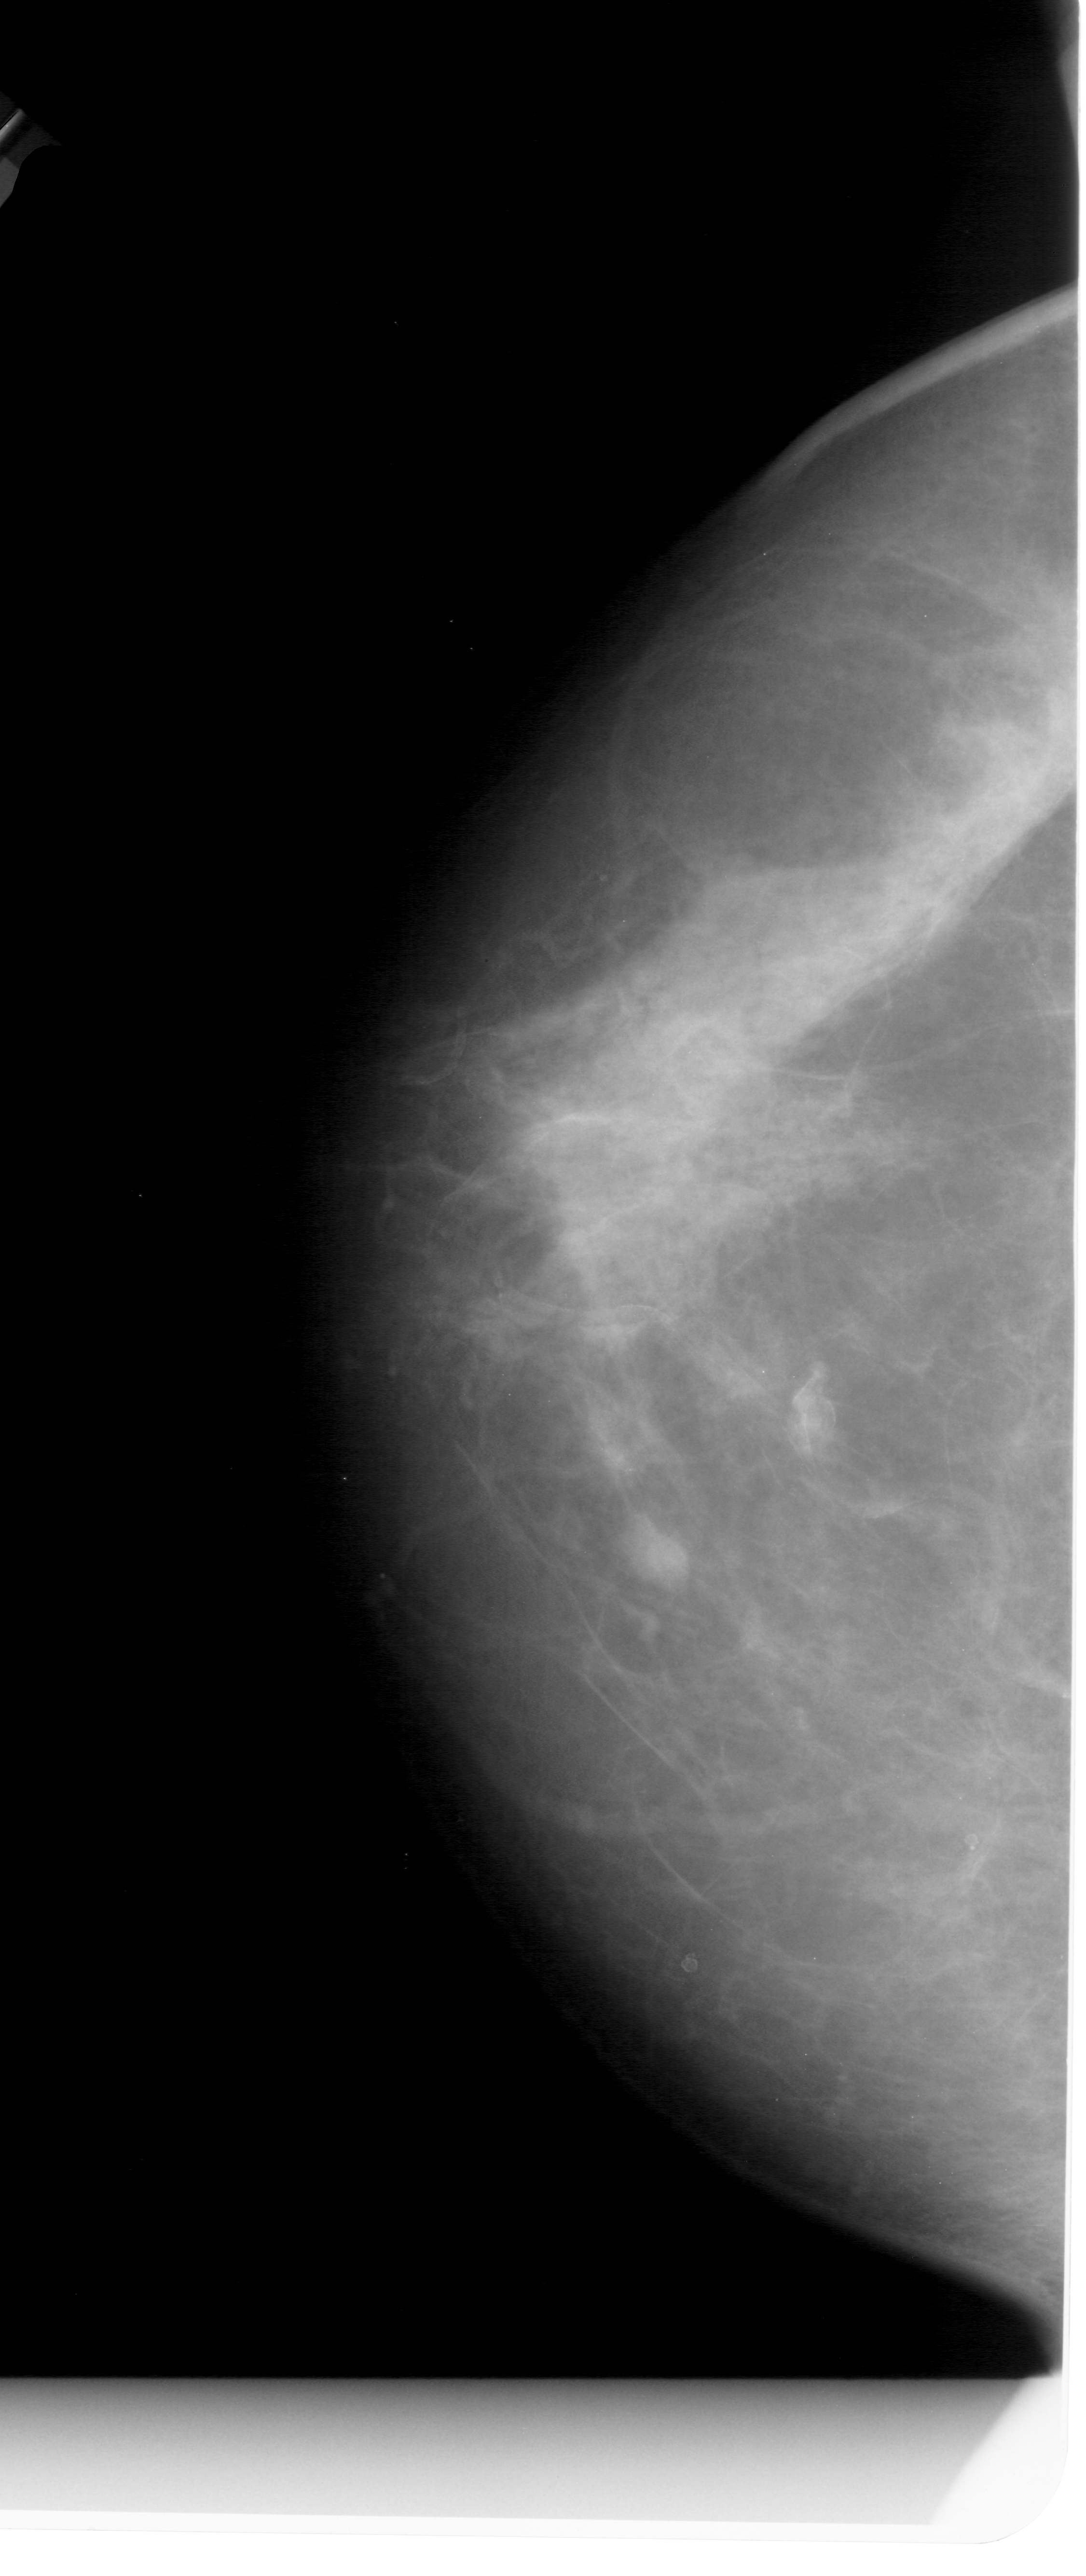
Mammogram (digitized film); left breast; craniocaudal (CC) view; BI-RADS breast density category 4 (scale 1–4).
Radiologist-marked abnormalities on this image: mass, shape irregular, margins ill defined; BI-RADS assessment category 4; pathology (as recorded): benign.